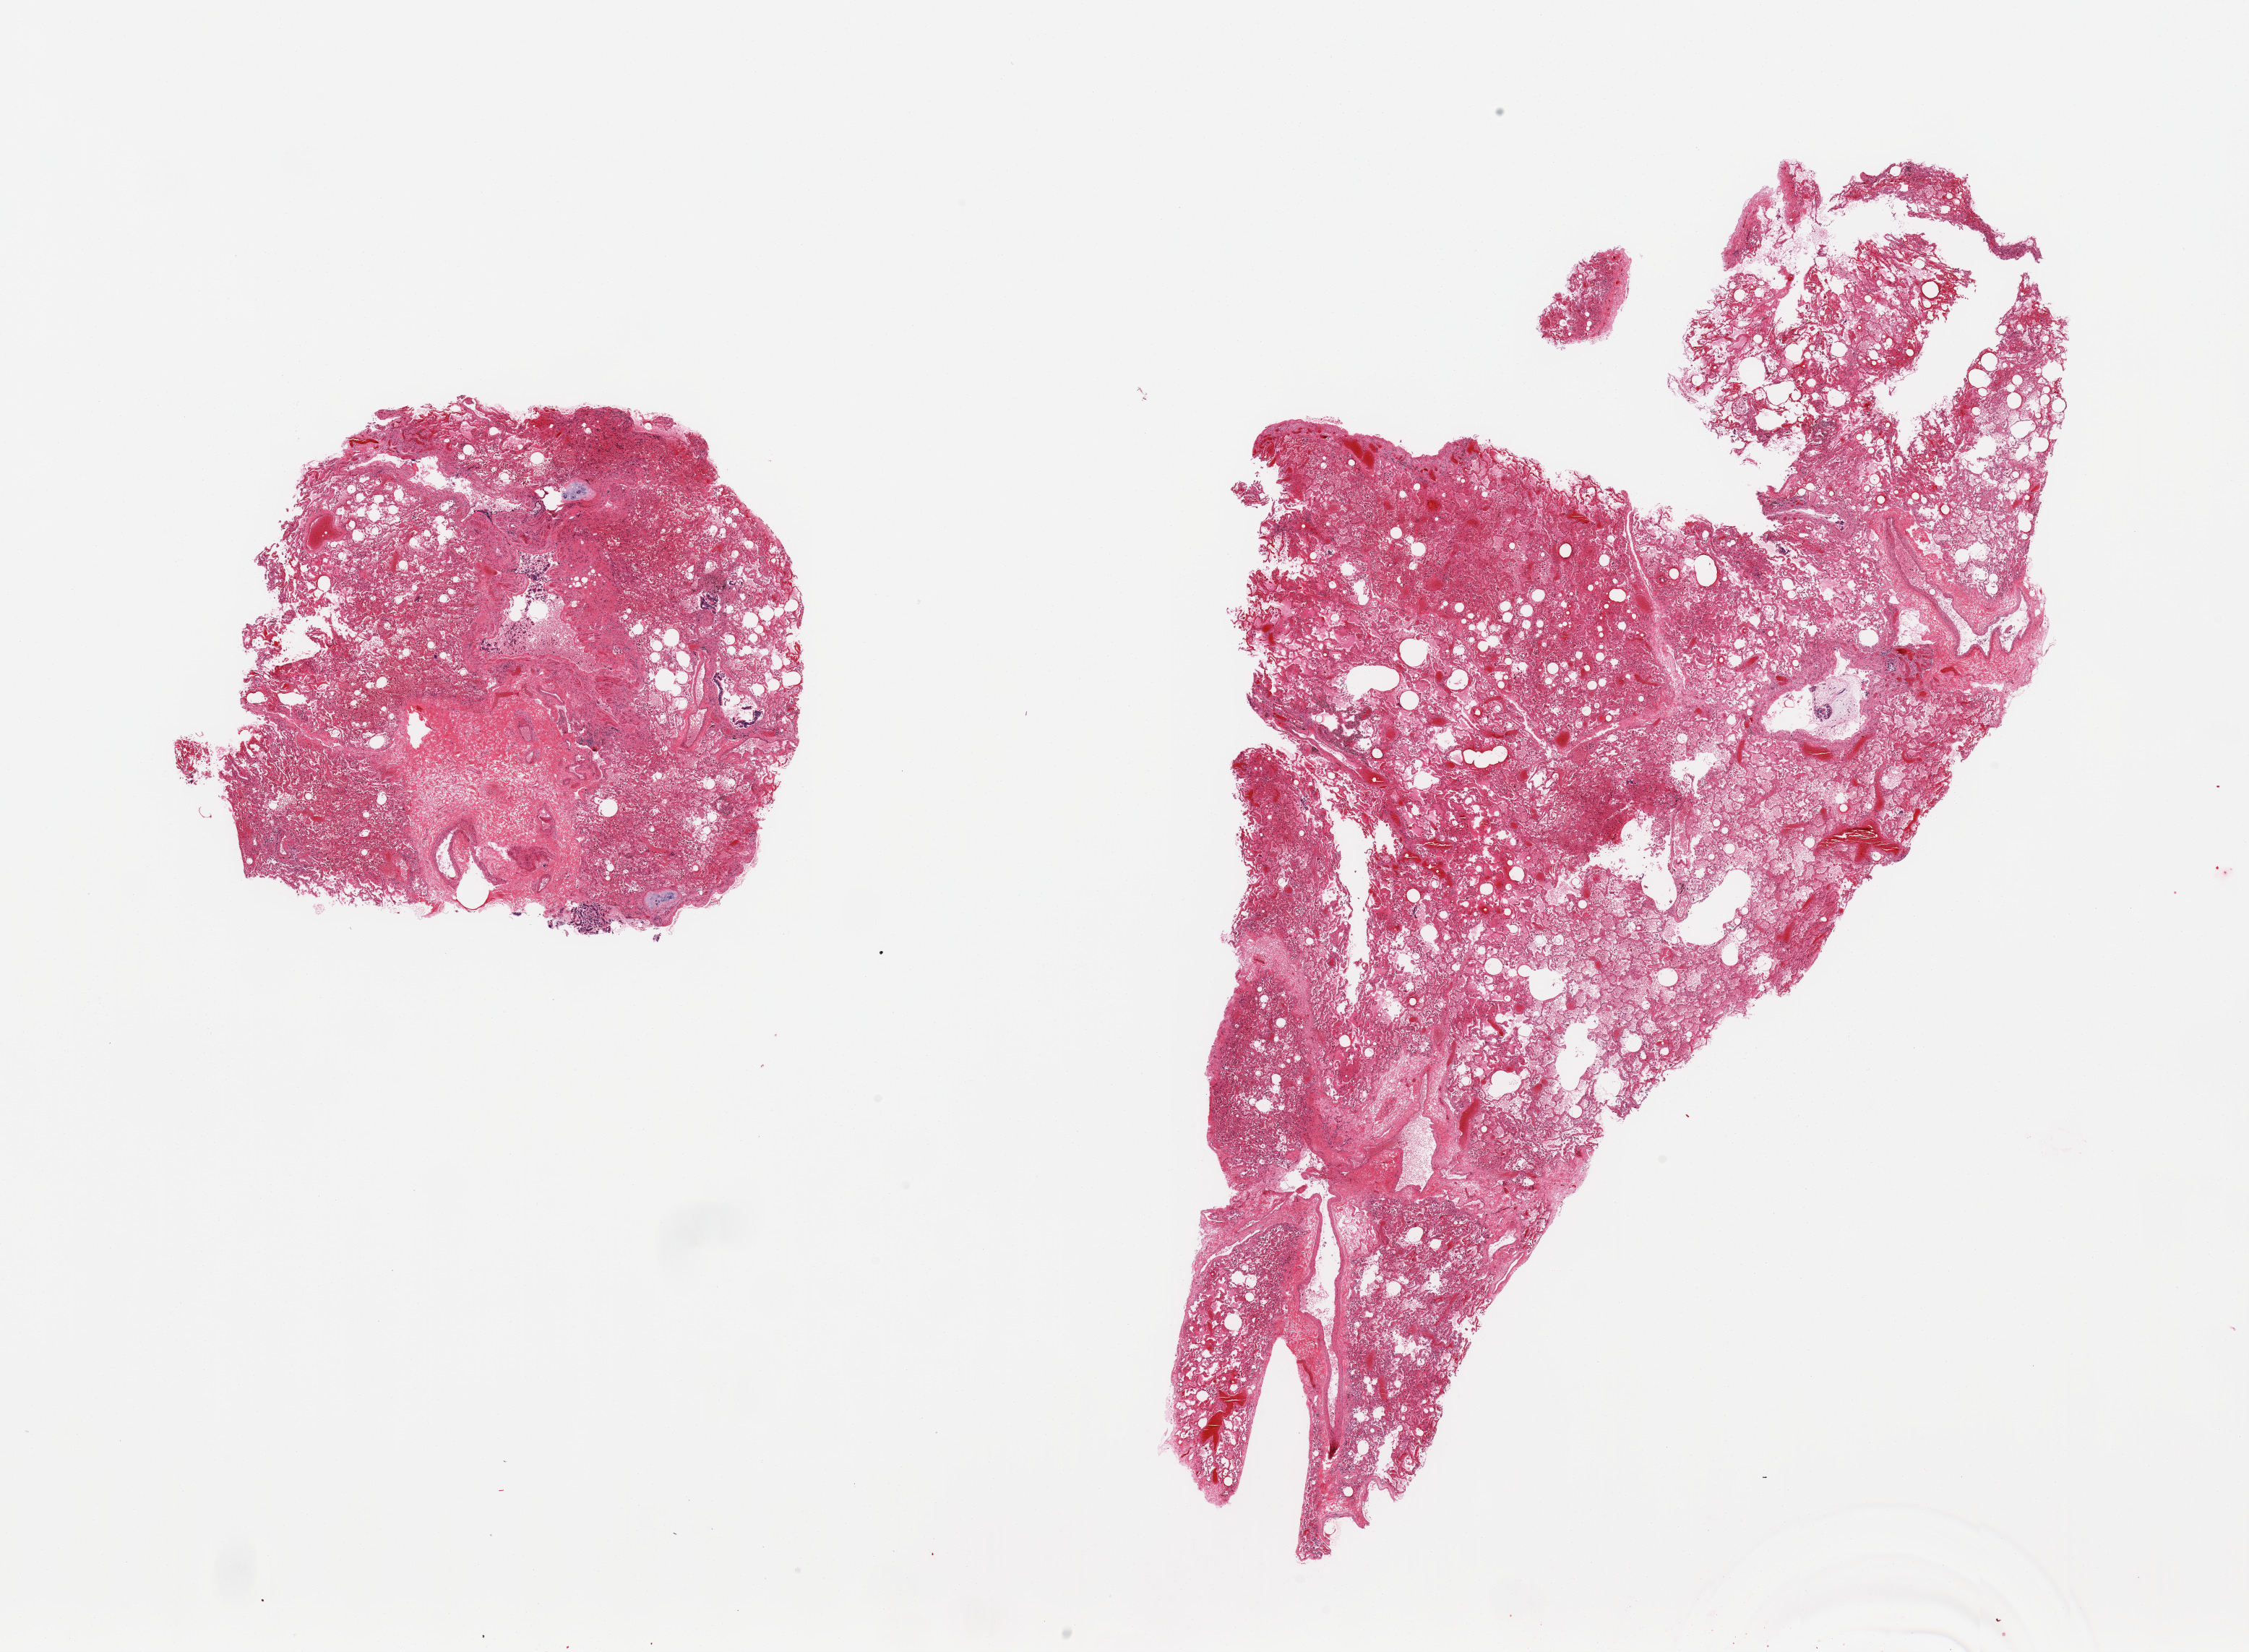
Haematoxylin and eosin whole-slide image — shown as a low-resolution overview of the whole scanned area (about 24.6 x 18.1 mm, acquisition: 20x scan); PAXgene-fixed paraffin-embedded (PFPE) section; target tissue: lung; donor tissue sample. Male donor.
Pathologist's review note for this sample: 2 pieces; moderate vascular congestion and alveolar edema, hemorrhage and macrophages.